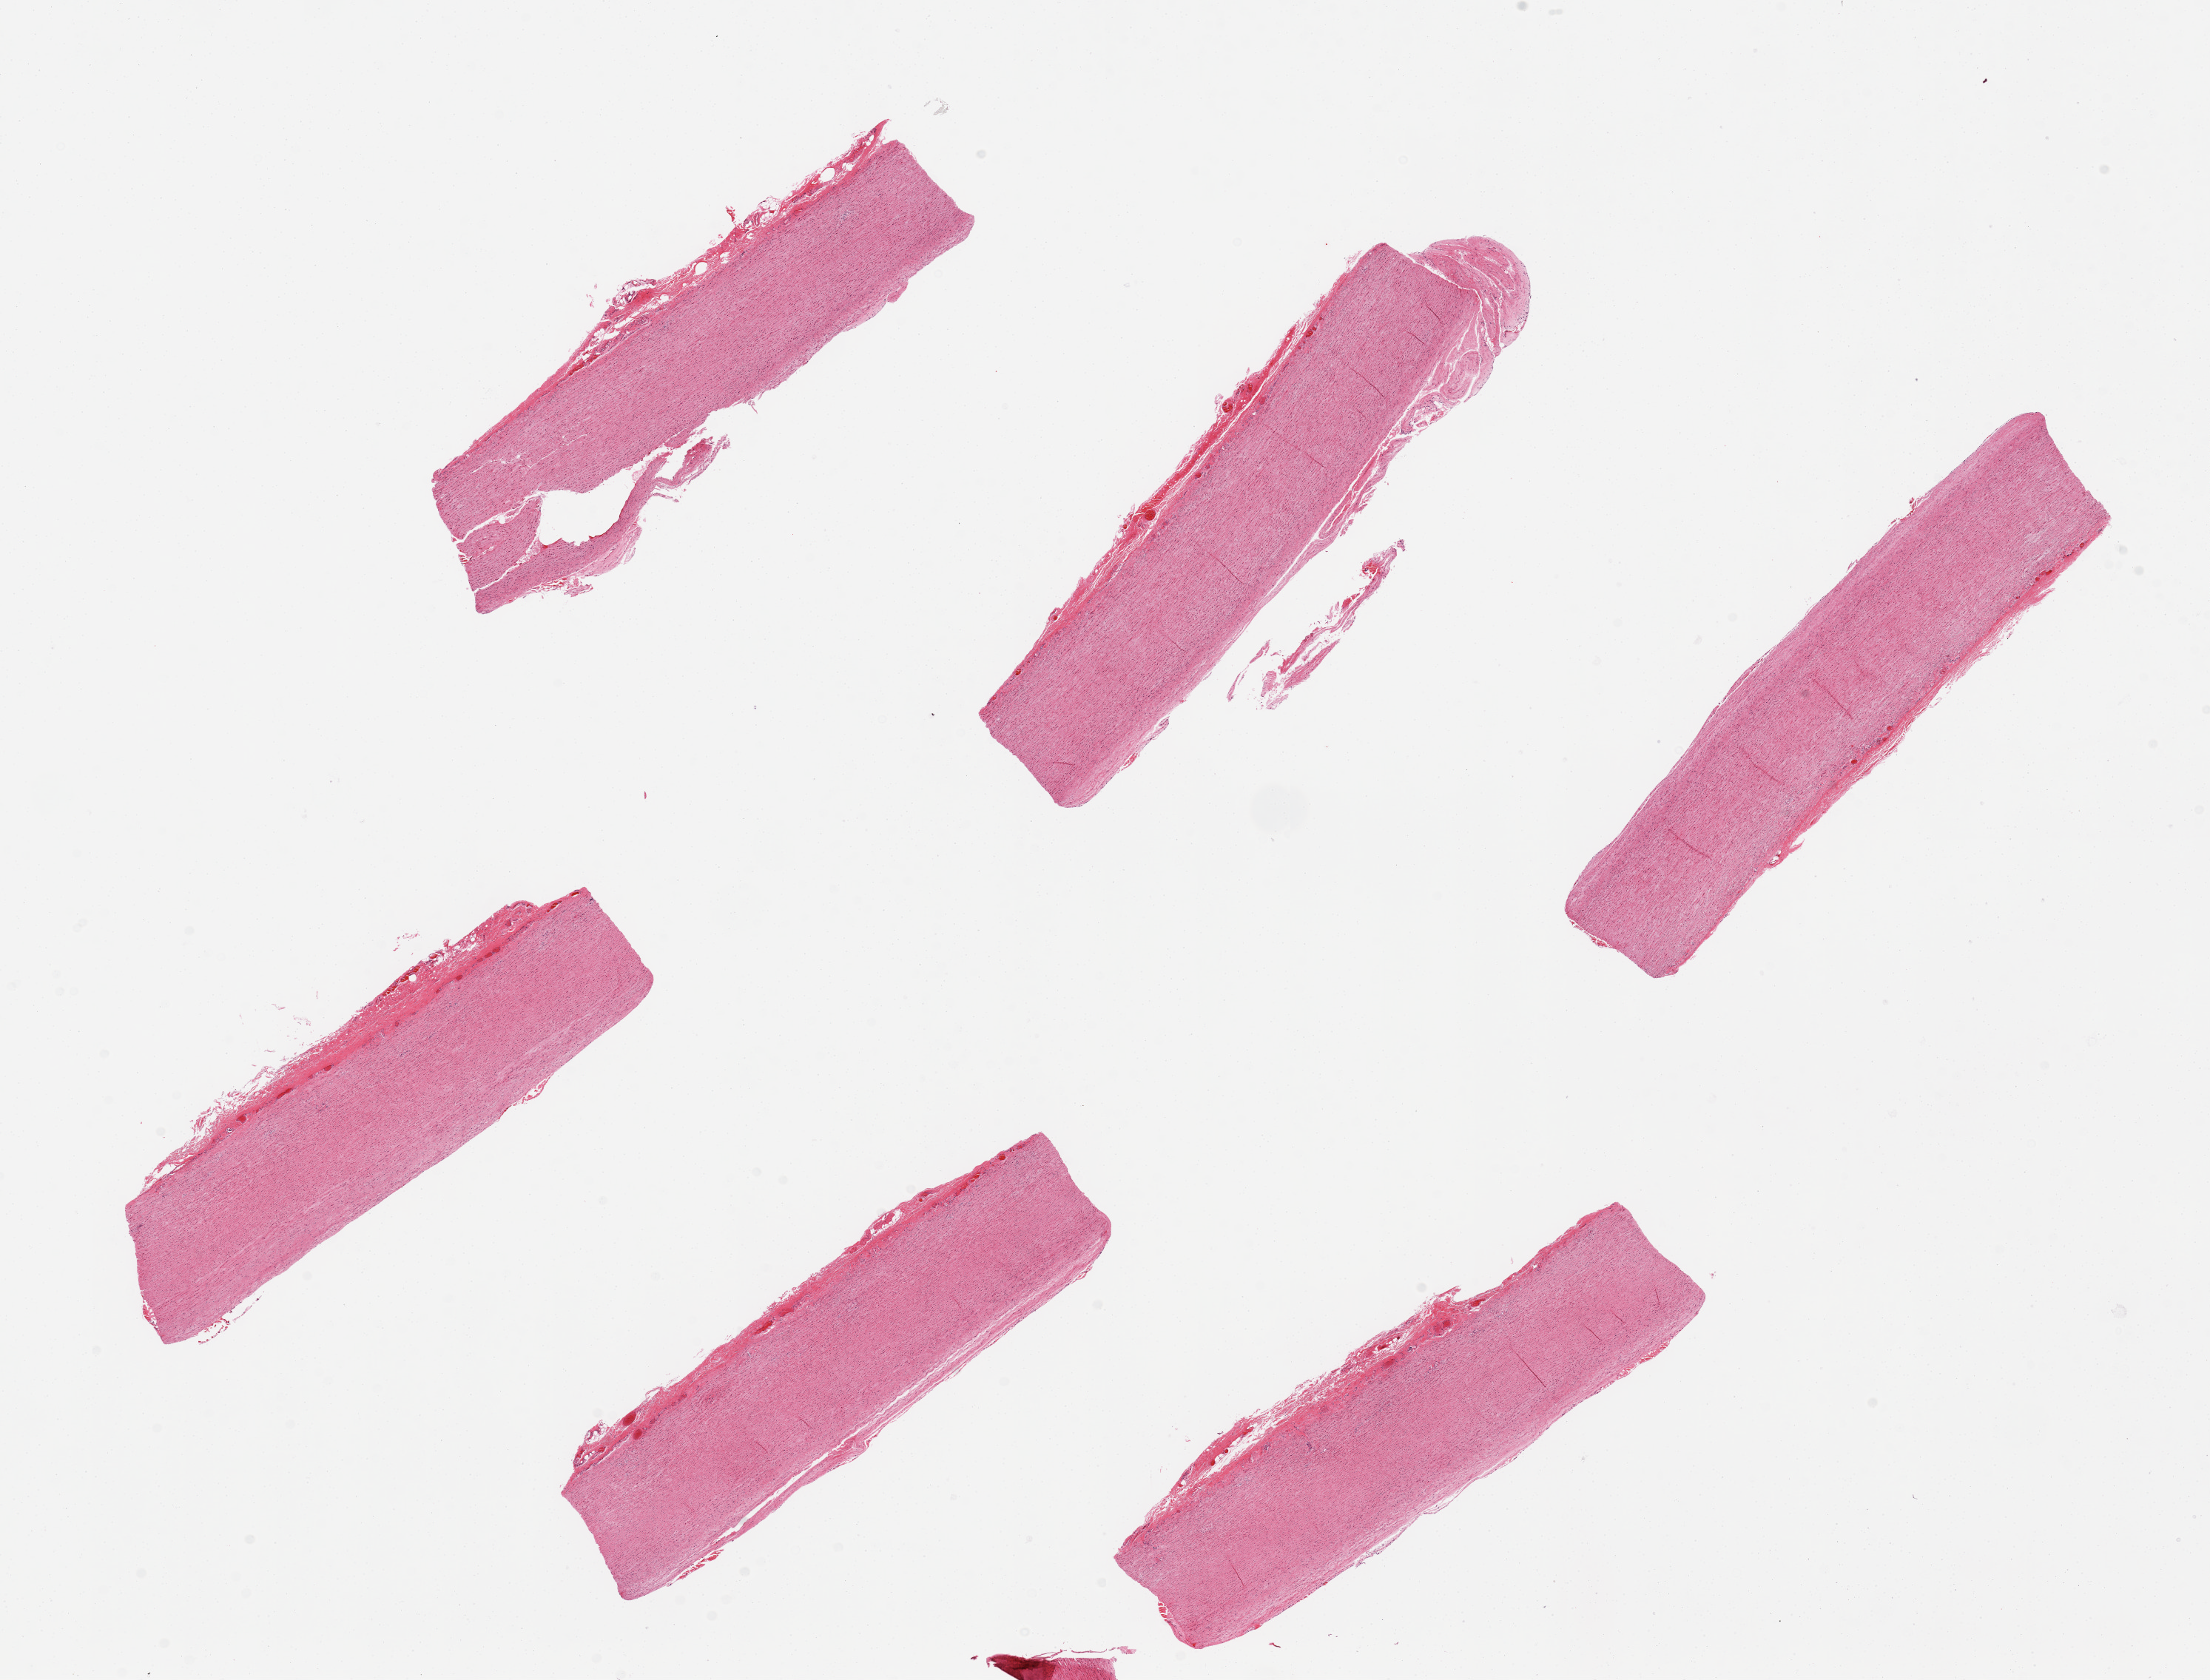
Digitized hematoxylin and eosin (H&E)-stained section, whole scanned area (about 23.6 x 18.0 mm) shown as a low-resolution overview, PAXgene-fixed paraffin-embedded (PFPE) section, section of aorta (target tissue), tissue donor sample. Donor: male.
Reviewer comment on this tissue sample: 6 pieces.